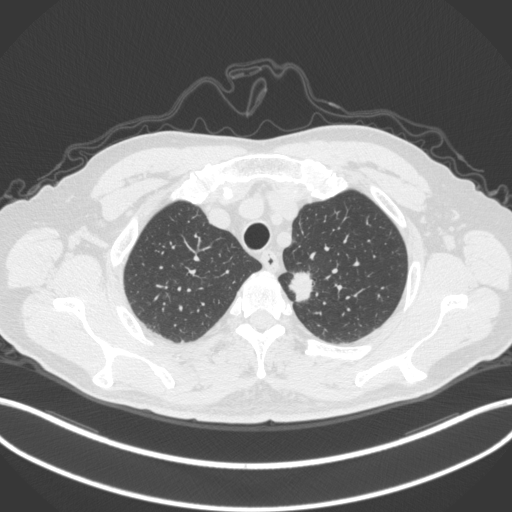
Chest CT, one axial slice; position 315 of 382 along the scan axis; 120 kVp; lung window (W 1500 / L -600 HU); 1 mm slice thickness; 512 × 512 image matrix, field of view 400 × 400 mm. Patient: male, 64 years. From the clinical record (not read from this slice): clinical TNM (as recorded): T1c N0 M0.
Structures marked on this image (bounding box drawn by a radiologist):
- lung tumour (recorded histology: adenocarcinoma): bounding box (x1, y1, x2, y2) in pixels: (283, 268, 315, 306)